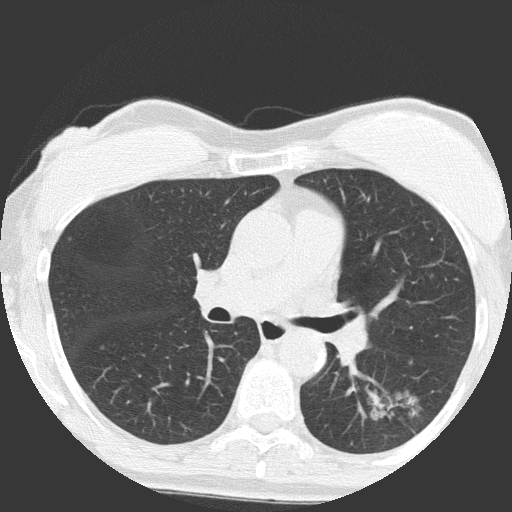
Low-dose screening chest CT, axial slice, baseline annual screen, lung window (W 1500 / L -600 HU), 2 mm slice thickness, lung (sharp) reconstruction kernel (FC51), 512 × 512 image matrix, field of view 300 × 300 mm. Female participant, aged 64 years at enrolment.
Expert-annotated lung lesion, box from (x=350, y=379) to (x=435, y=453) px. Screening reader's record for this exam (one nodule recorded; not confirmed to be the boxed lesion): non-calcified nodule or mass ≥4 mm, right upper lobe, 4 × 4 mm, poorly defined margins, ground glass attenuation. Note: the box lies in the patient's left hemithorax on this image, whereas the reader's record names the right lung; they may be different findings. Official screen result: positive, change unspecified: nodule(s) >= 4 mm or enlarging nodule(s), mass(es), or other non-specific abnormalities suspicious for lung cancer. Later outcome: lung cancer diagnosed 932 days after this screen (after the third annual screen) — adenocarcinoma, NOS, left lower lobe, moderately differentiated (G2), stage IA (AJCC 6th edition), 17 mm at pathology.